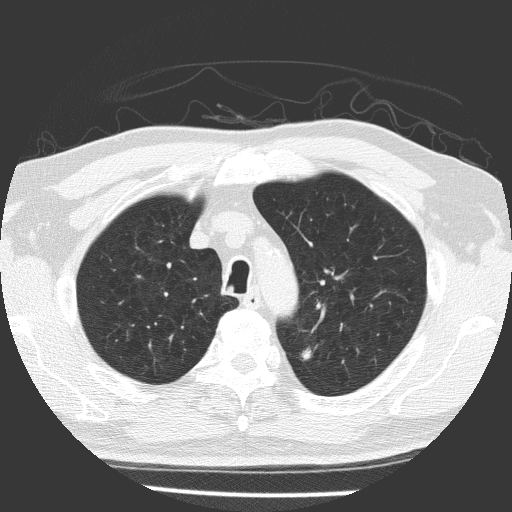
Low-dose screening chest CT, one axial slice. Slice 132 of 169 in the series (ordered by position). Reconstruction kernel FC51. 120 kVp. Lung window (W 1500 / L -600 HU). 512 × 512 image matrix.
Structures marked on this image (expert manual segmentation):
- lesion 1 (tumor, upper lobe of left lung): box from (x=301, y=348) to (x=311, y=360) px